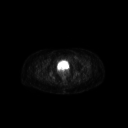
FDG PET of an extremity soft-tissue mass (from a PET/CT study), one axial slice. Slice 58 of 267 in the series (ordered by position). 3.27 mm slice thickness. 128 × 128 image matrix, field of view 700 × 700 mm. Female patient, age 47 years. From the clinical record (not read from this slice): histological type: myxofibrosarcoma; grade: intermediate; site of the primary tumour: left thigh.
Outlined on this slice (expert contour drawn on MRI and transferred to this co-registered scan by the dataset authors):
- gross tumour volume including surrounding oedema: bounding box <69,58,82,63> (left, top, right, bottom; pixels)